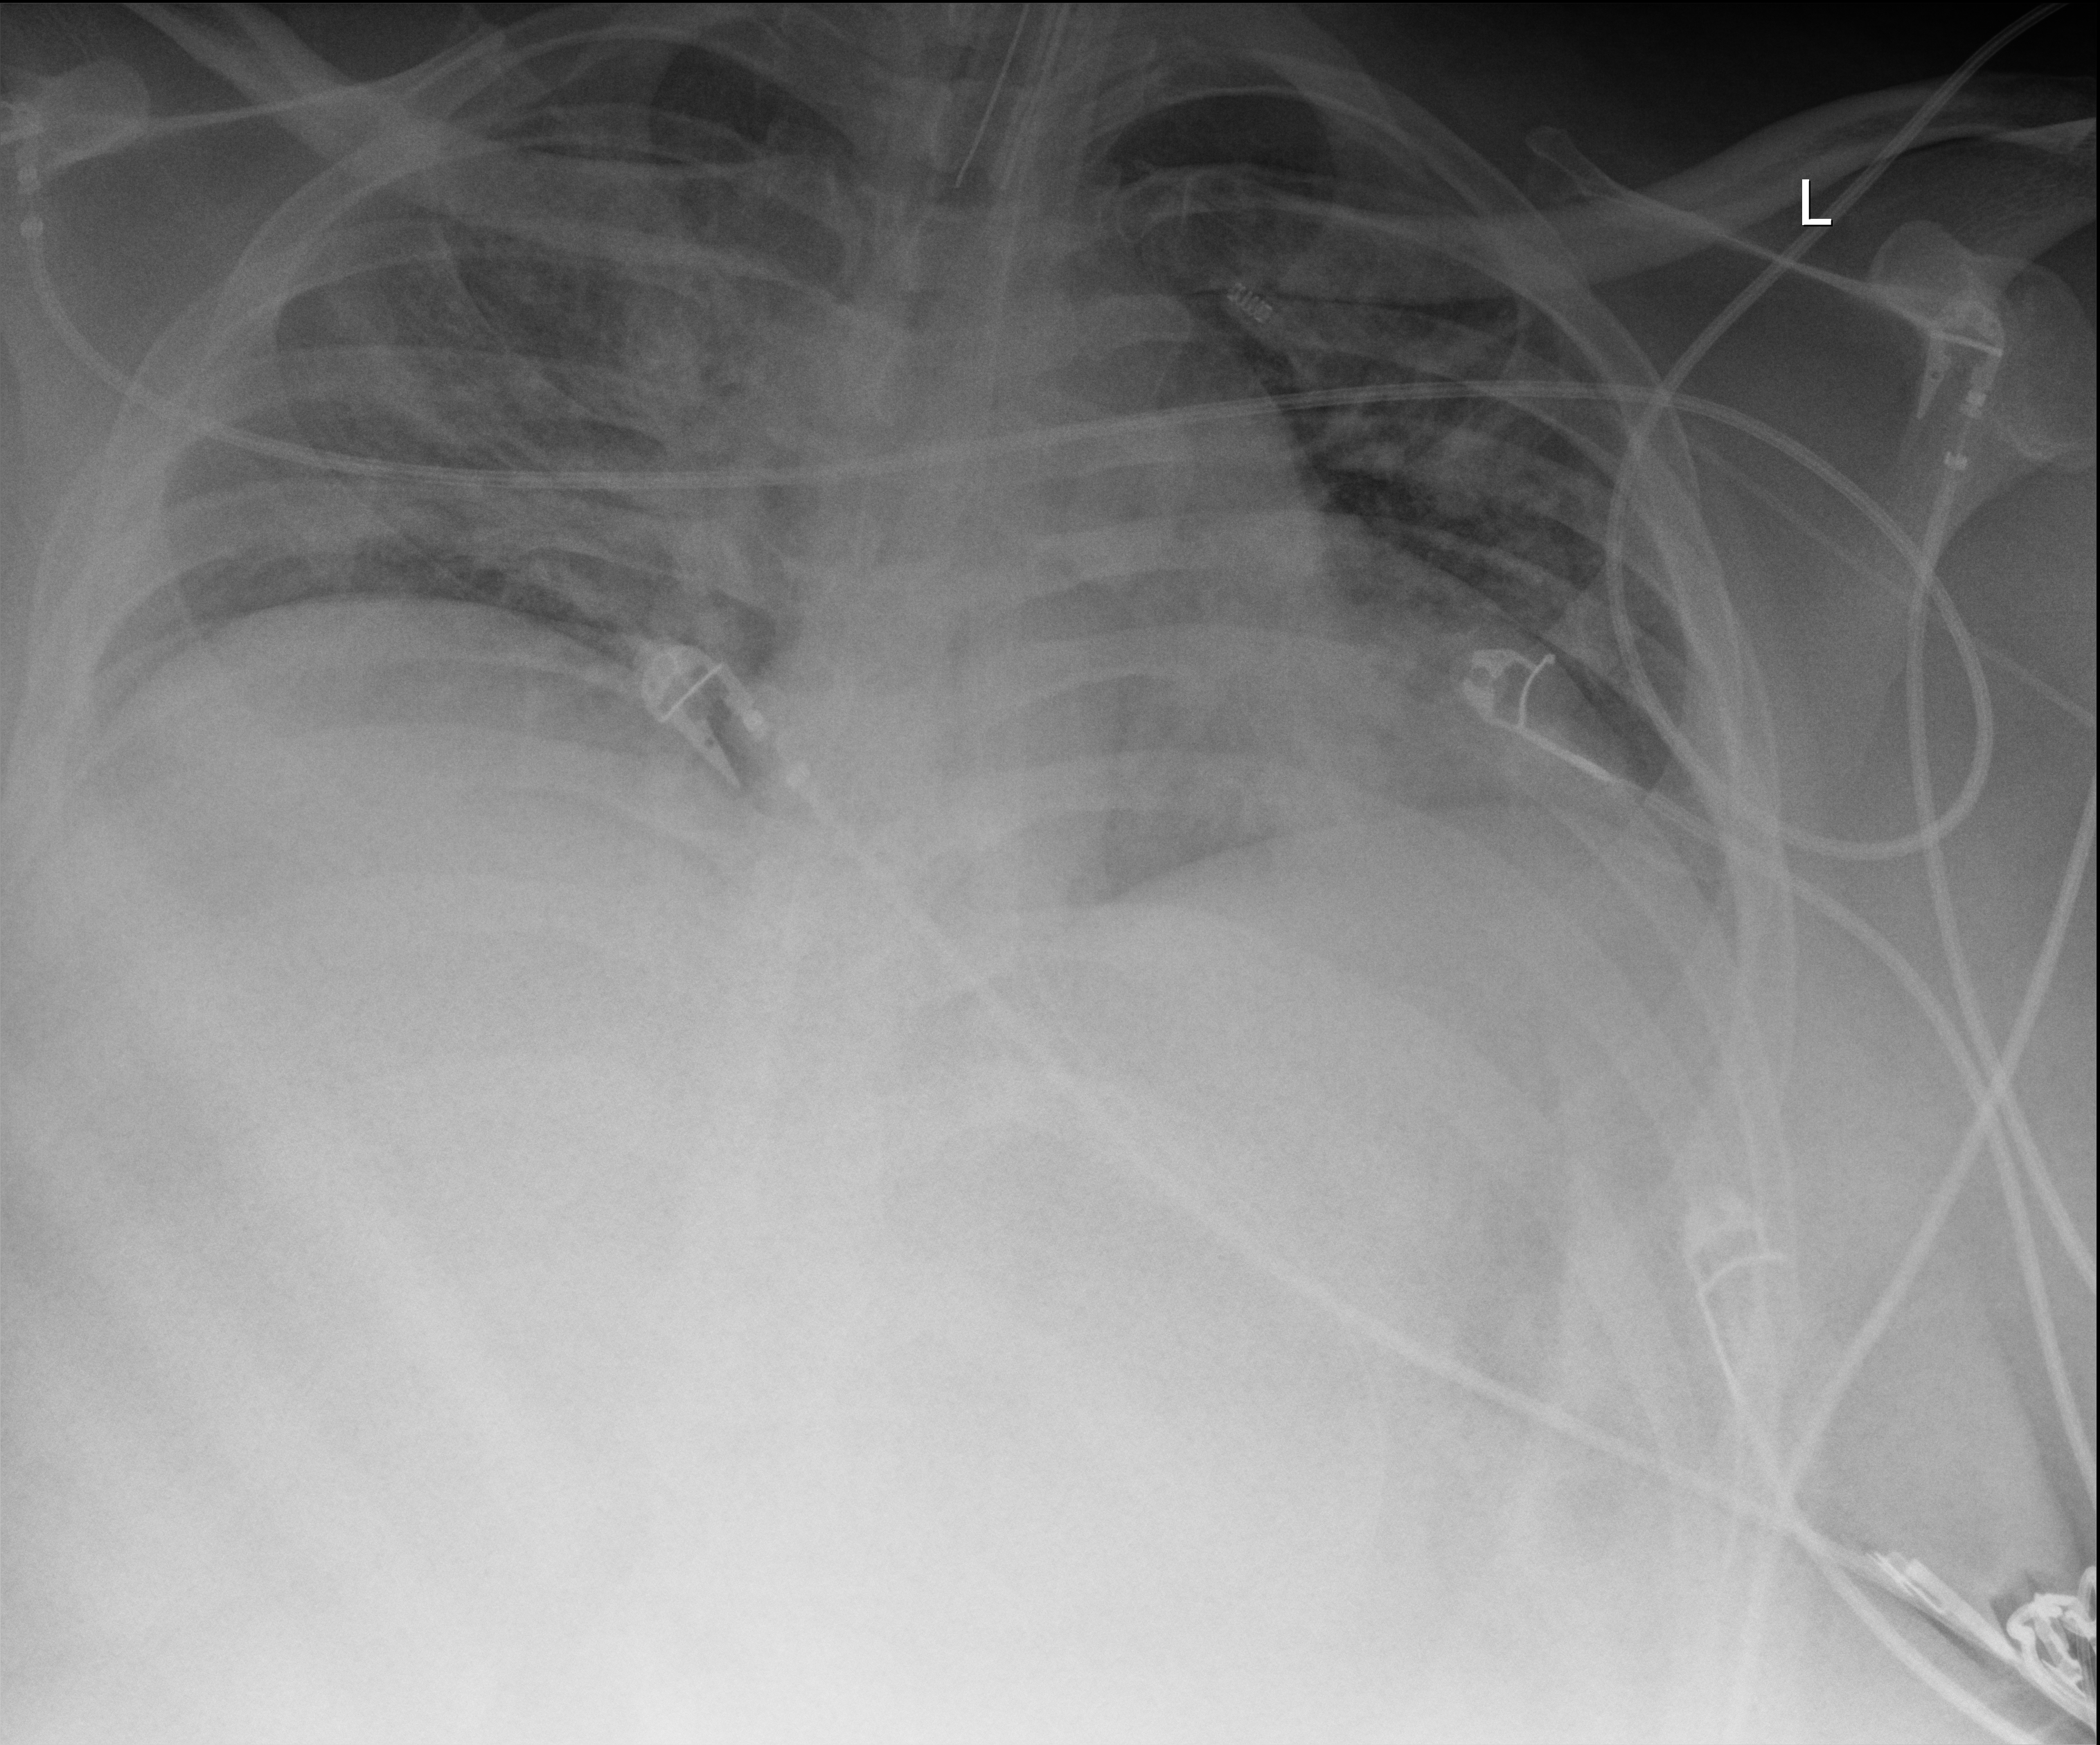
Chest X-ray (portable), anteroposterior (AP) projection. Patient hospitalised with COVID-19; male, aged 18–59 years.
Admission-level facts for this patient (not findings on this image; timing relative to this image not recorded):
- mechanically ventilated during this hospital stay: yes
- COPD (admission record): yes
- admitted to intensive care during this hospital stay: yes